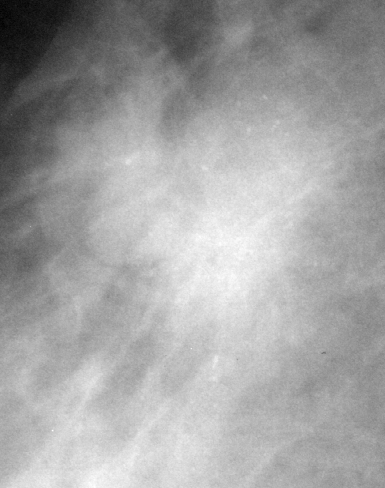
Region of interest cut from a scanned film mammogram (one marked finding), right breast, MLO view.
Mass, shape irregular, margins spiculated; BI-RADS assessment category 5; pathology (as recorded): malignant.